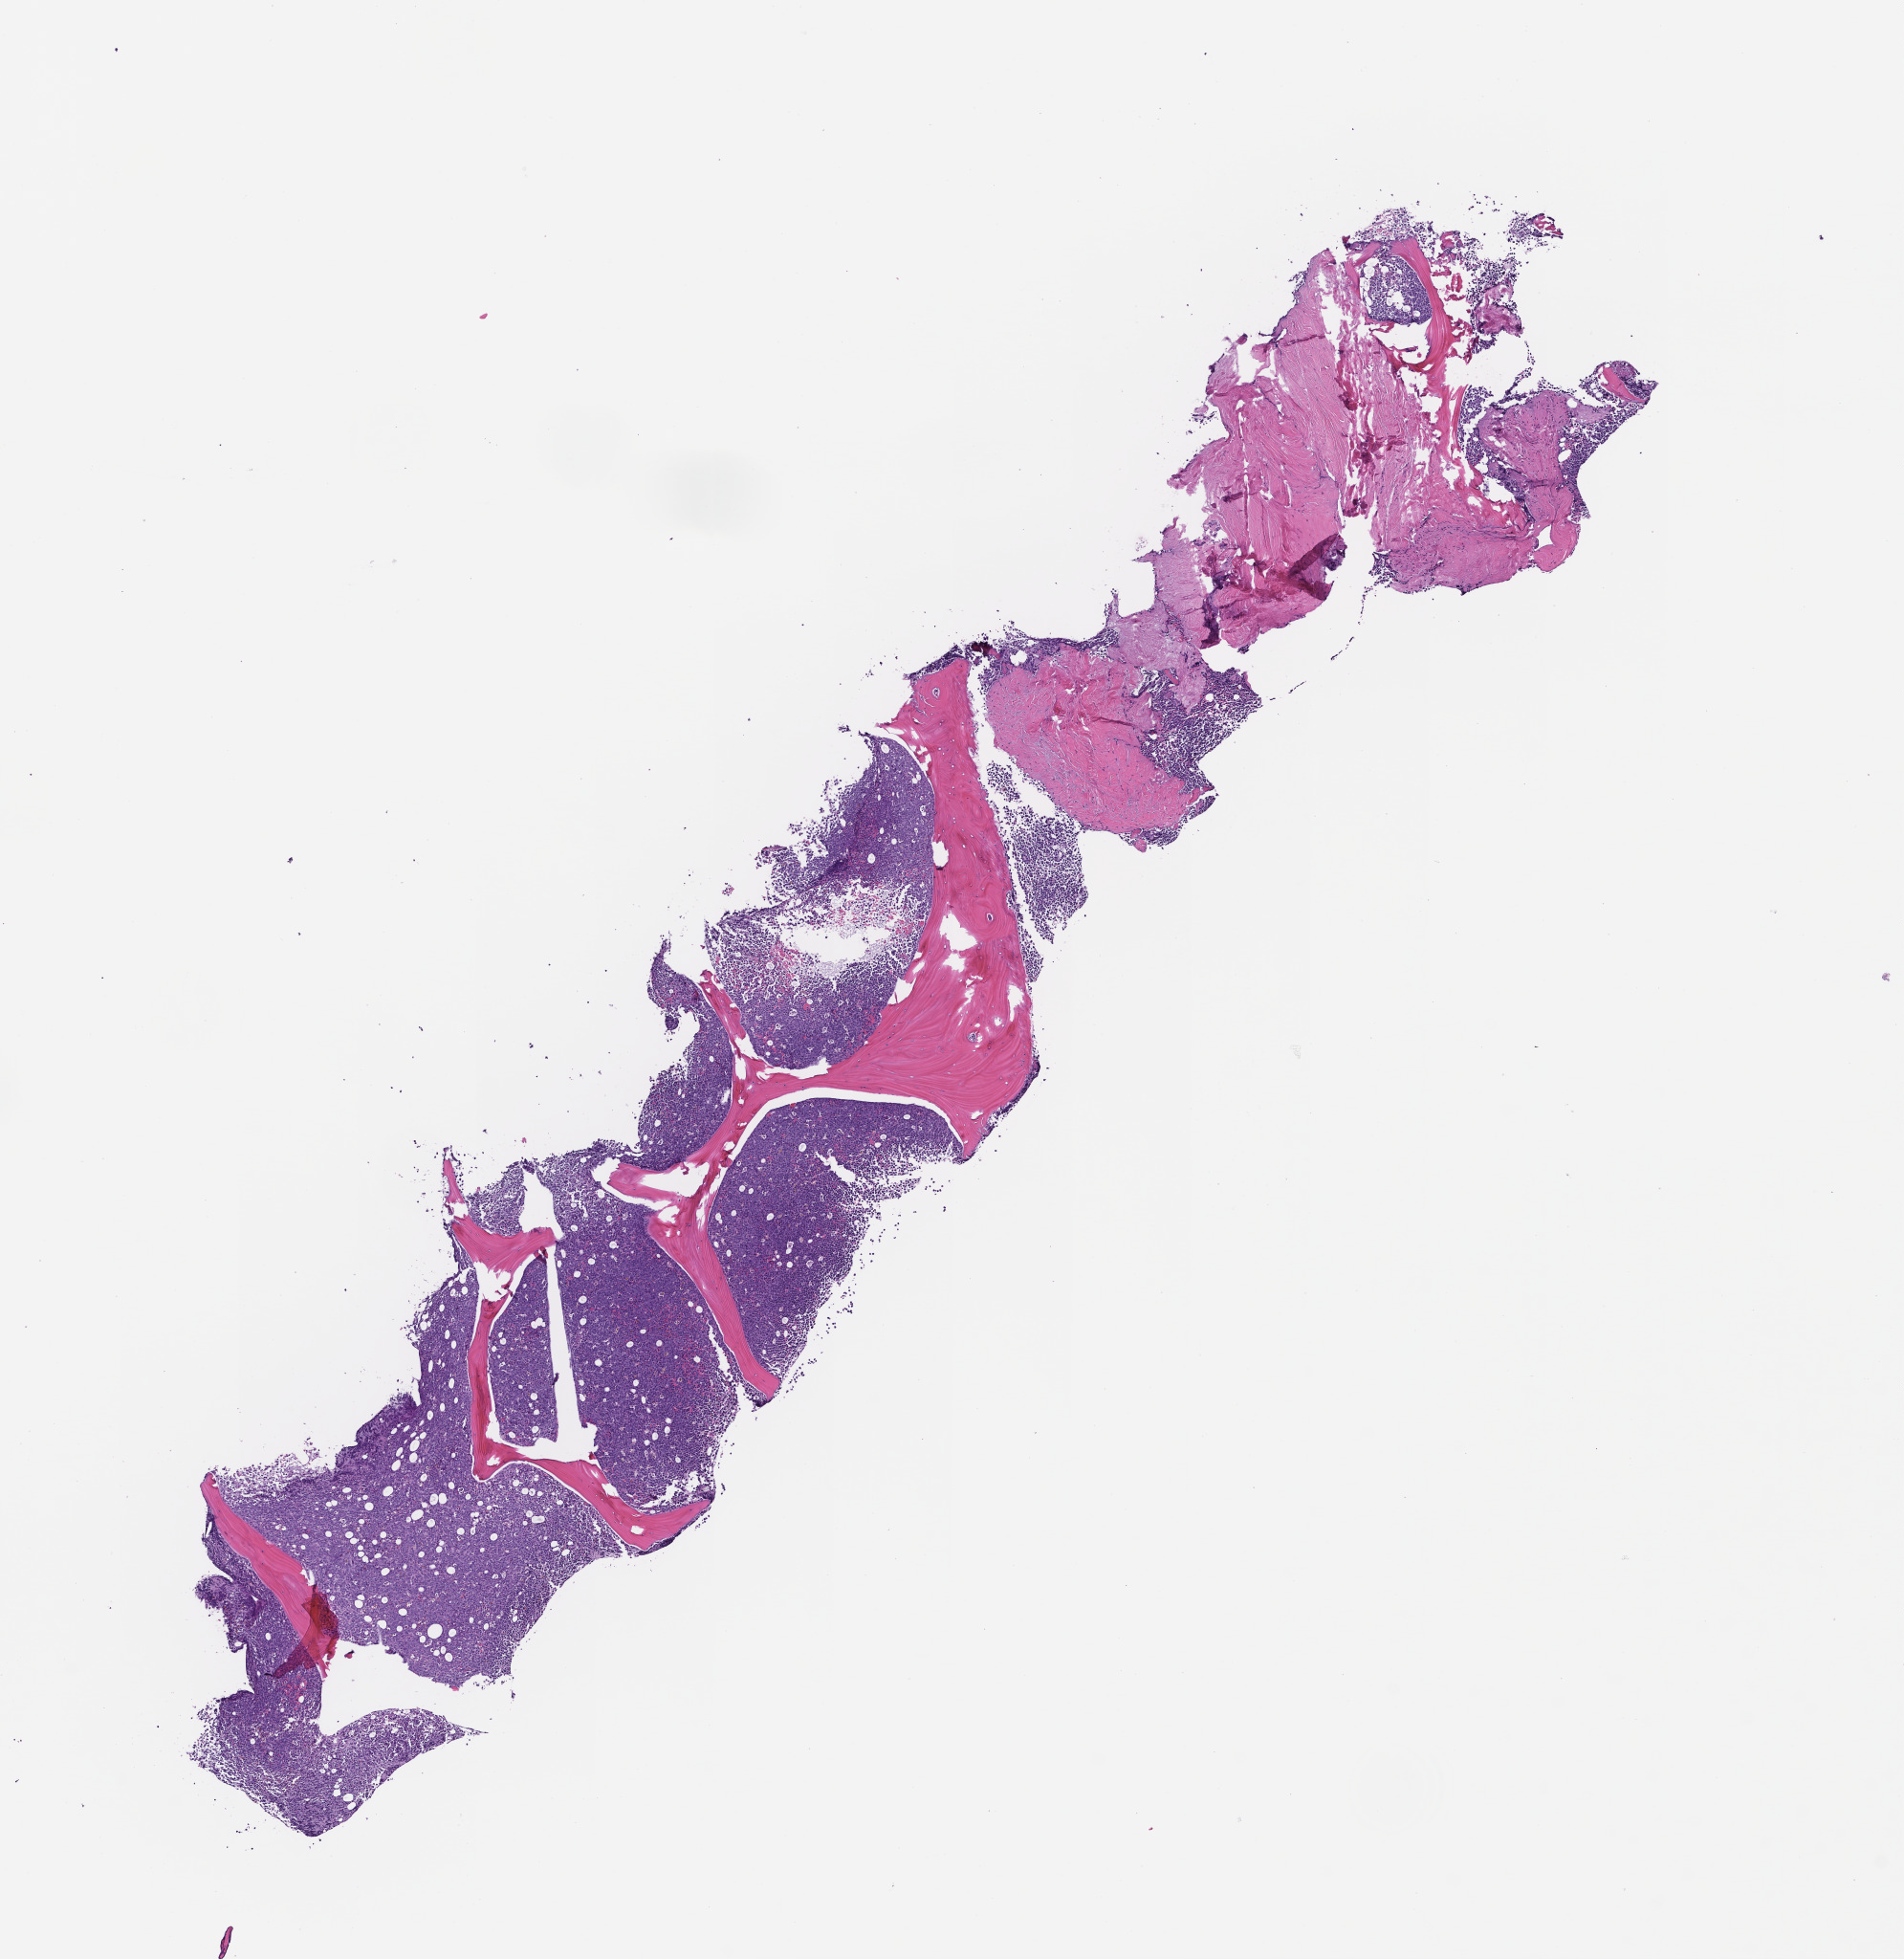
Whole-slide image, hematoxylin and eosin (H&E) stain, shown as a low-resolution overview of the whole scanned area (about 8.0 x 8.3 mm). Formalin-fixed paraffin-embedded section. Site: bone marrow. Specimen time point: collected at baseline (before treatment). Patient: male.
- this section: primary tumour tissue
- diagnosis: Acute Myeloid Leukemia Not Otherwise Specified